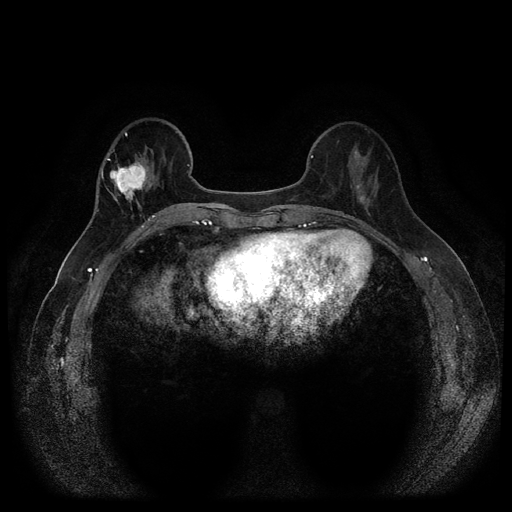
Breast MRI (dynamic contrast-enhanced, multi-phase), one axial slice. Position 35 of 116 along the scan axis. Dynamic contrast-enhanced series, time point 2 of 5 at this slice position (early post-contrast). 1.5 T. TE 2.6 ms, TR 5.4 ms. 512 × 512 image matrix, field of view 340 × 340 mm. Patient: female, 56 years.
Outlined on this slice (semi-automatic segmentation, software-assisted and operator-edited):
- breast lesion (labelled benign in the annotation): box from (x=354, y=150) to (x=365, y=163) px
- breast lesion (labelled 'tumour' in the annotation; benign lesions carry a separate 'benign' label): (x=108, y=155)–(x=155, y=203)